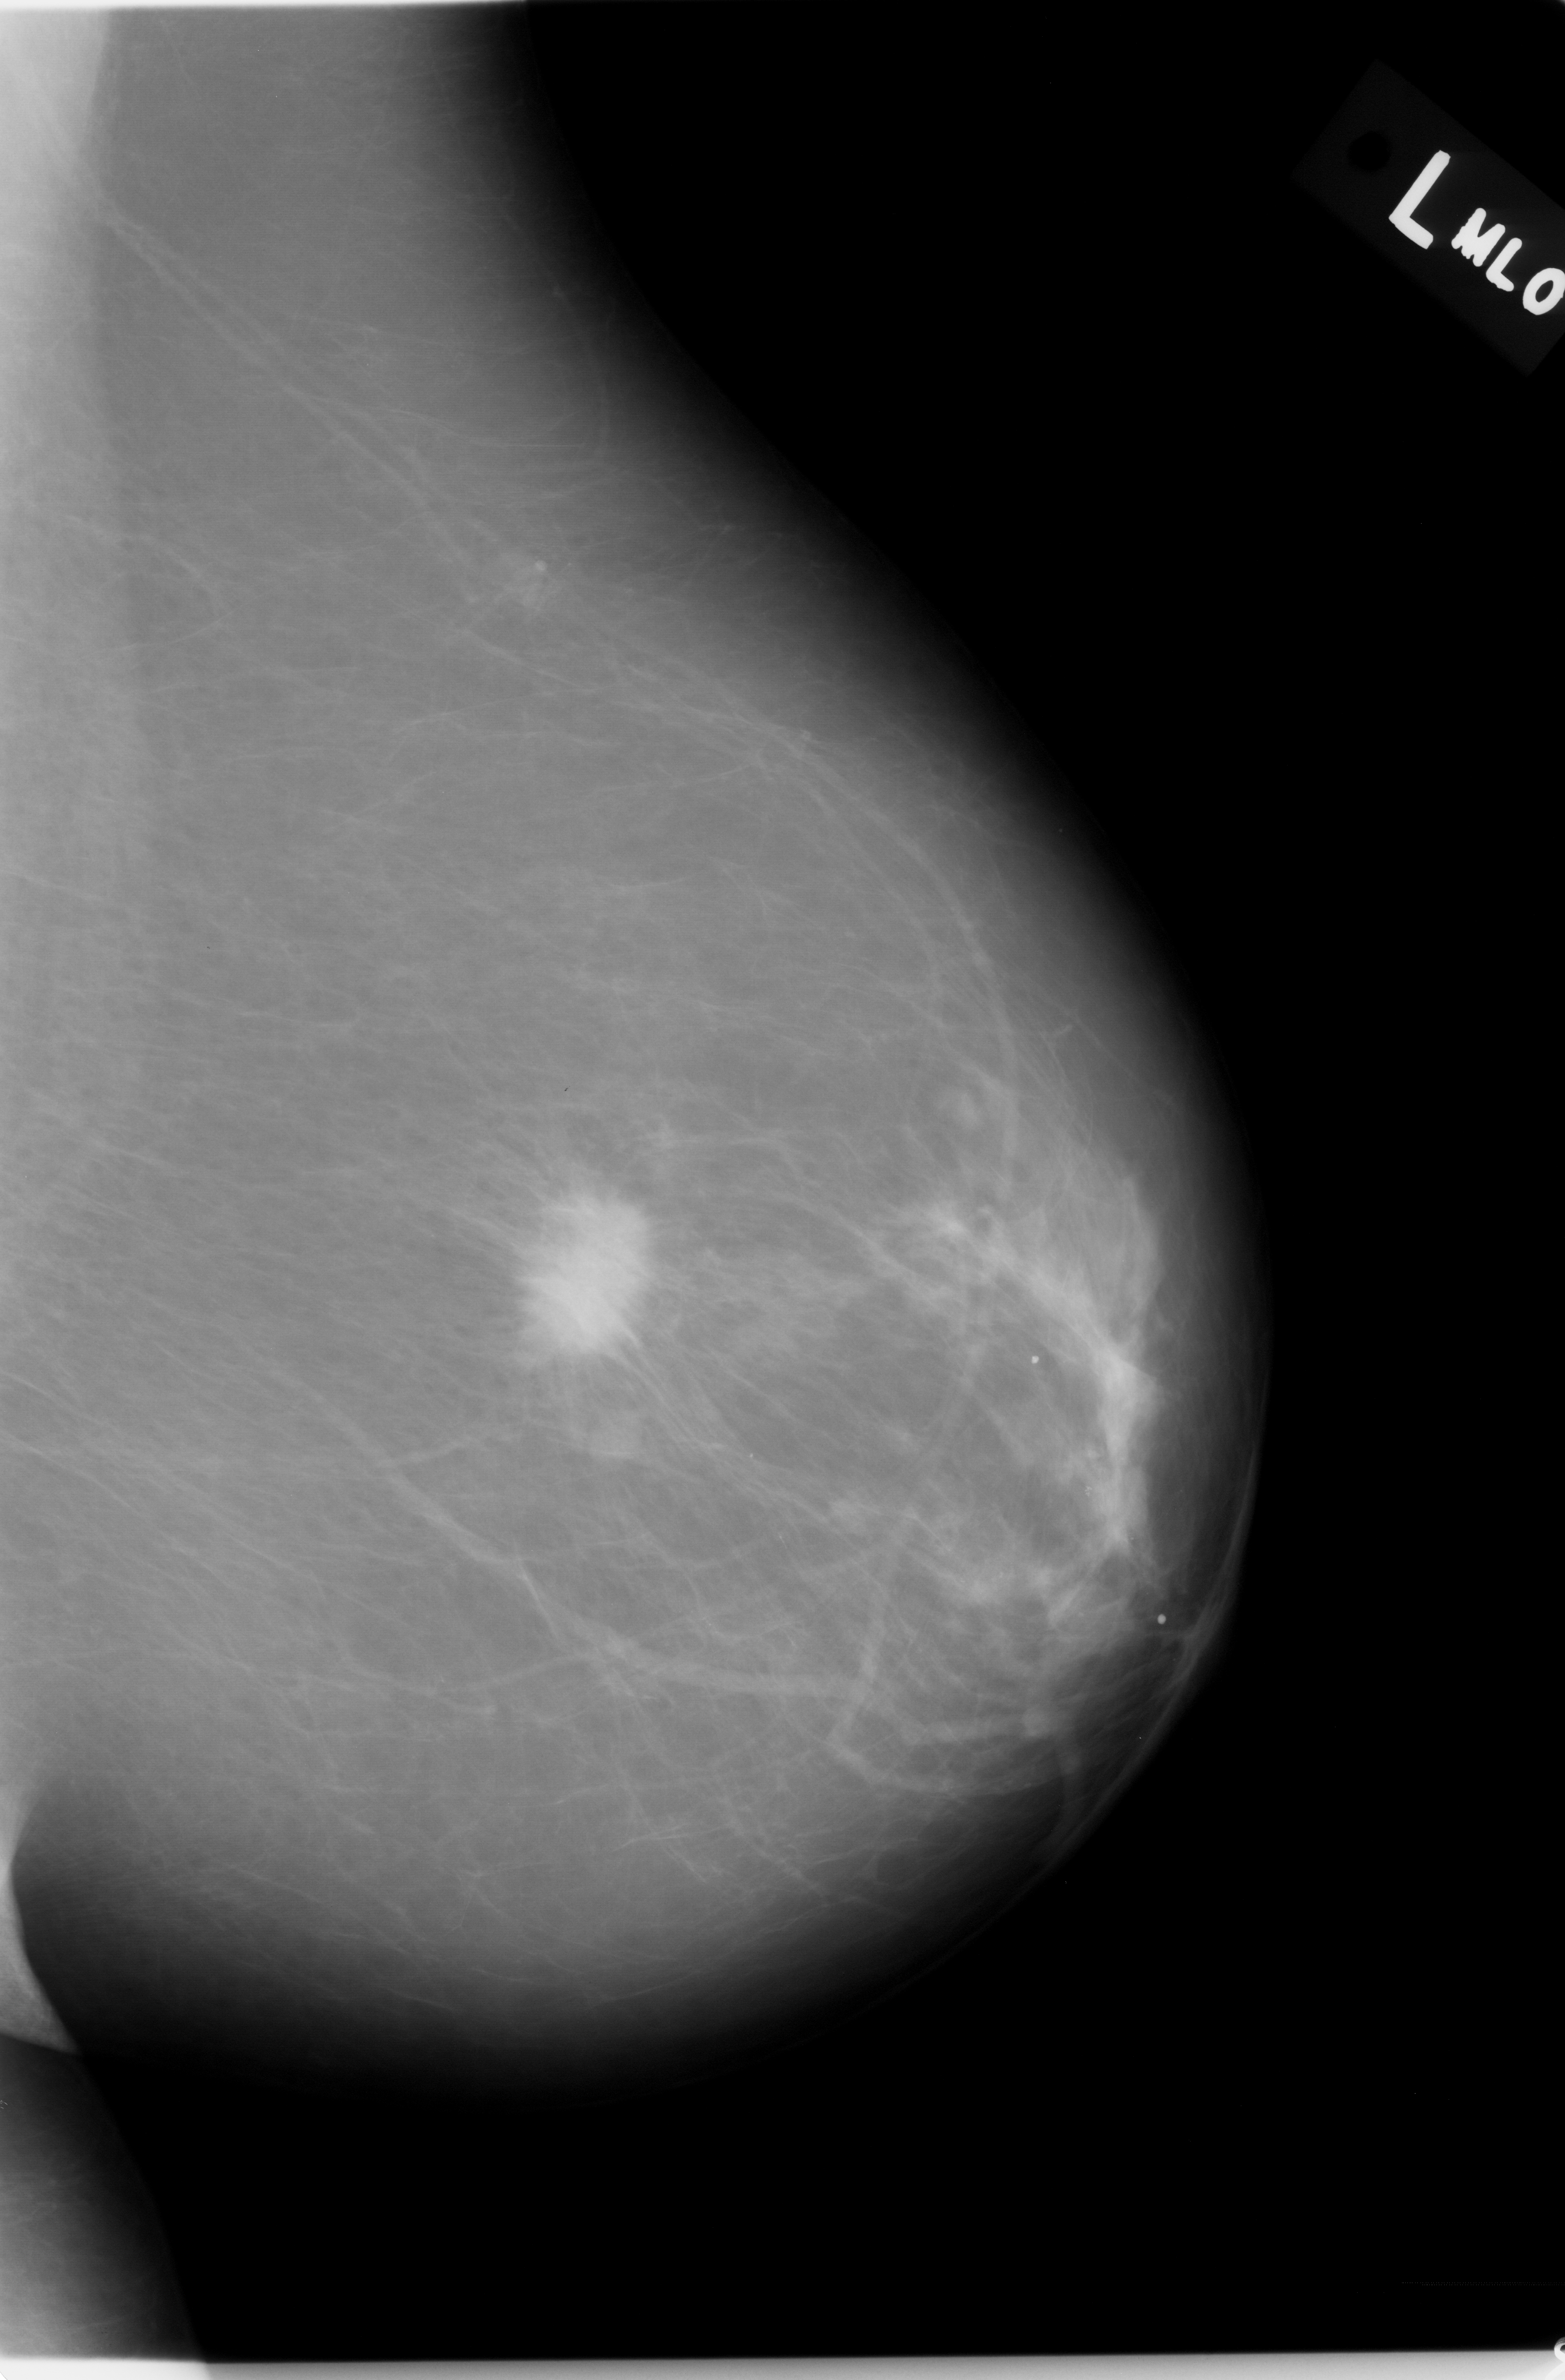
Scanned film-screen mammogram, left breast, mediolateral oblique (MLO) view.
Mass, shape irregular, margins spiculated; BI-RADS assessment category 5; subtlety rating 5 on a 1 (subtle) to 5 (obvious) scale; pathology result (as recorded, not read from the image): malignant.